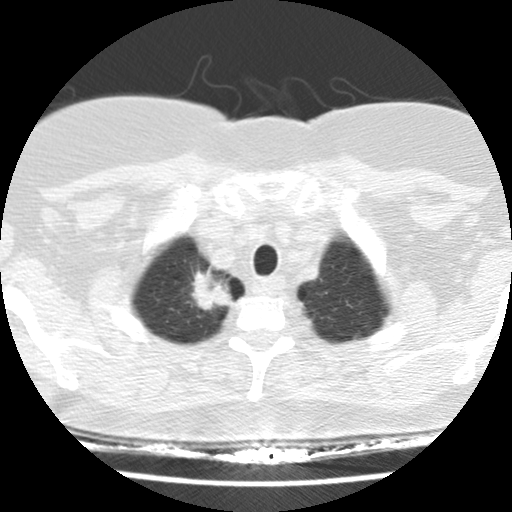
Low-dose screening chest CT, one axial slice; slice 134 of 148 in the series (ordered by position); reconstruction kernel STANDARD; 120 kVp; lung window (W 1500 / L -600 HU); 2.5 mm slice thickness; 512 × 512 image matrix.
Structures marked on this image (manually delineated by an expert):
- lesion 1 (tumor, upper lobe of right lung): box from (x=191, y=271) to (x=231, y=310) px